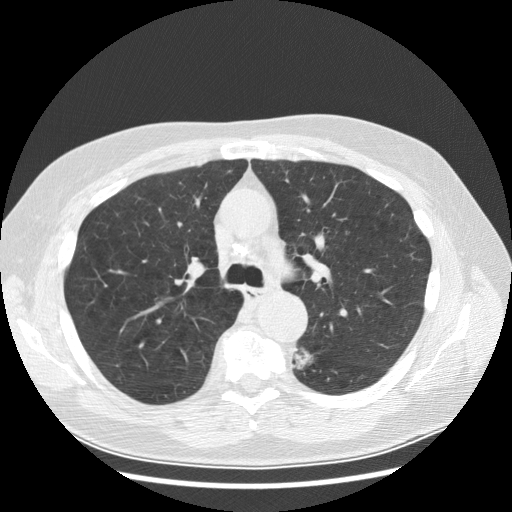
Low-dose screening chest CT, one axial slice; 120 kVp; lung window (W 1500 / L -600 HU); 512 × 512 image matrix, field of view 370 × 370 mm.
Annotated regions visible in this slice (expert manual segmentation):
- lesion 1 (tumor, lower lobe of left lung): bounding box [x1, y1, x2, y2] px = [295, 348, 312, 369]